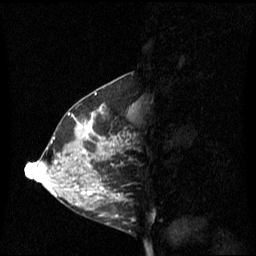
Breast MRI (dynamic contrast-enhanced), one sagittal slice; position 27 of 60 along the scan axis; dynamic contrast-enhanced series, image 2 of 3 at this slice position (ordered by acquisition); 1.5 T; TE 4.2 ms, TR 8.4 ms; 256 × 256 image matrix. Patient: female, 42 years. From the clinical record (not read from this slice): setting: breast cancer imaged before/during neoadjuvant chemotherapy; receptor status: HR-positive, HER2-negative.
Outlined on this slice (semi-automatically segmented with operator editing):
- analysis volume of interest (the breast-tissue region the enhancement analysis was run in; not a lesion): box from (x=68, y=106) to (x=135, y=201) px
- tumour enhancement mask (voxels above the 70 % enhancement threshold inside the analysis volume of interest): (x=80, y=110)–(x=119, y=199)